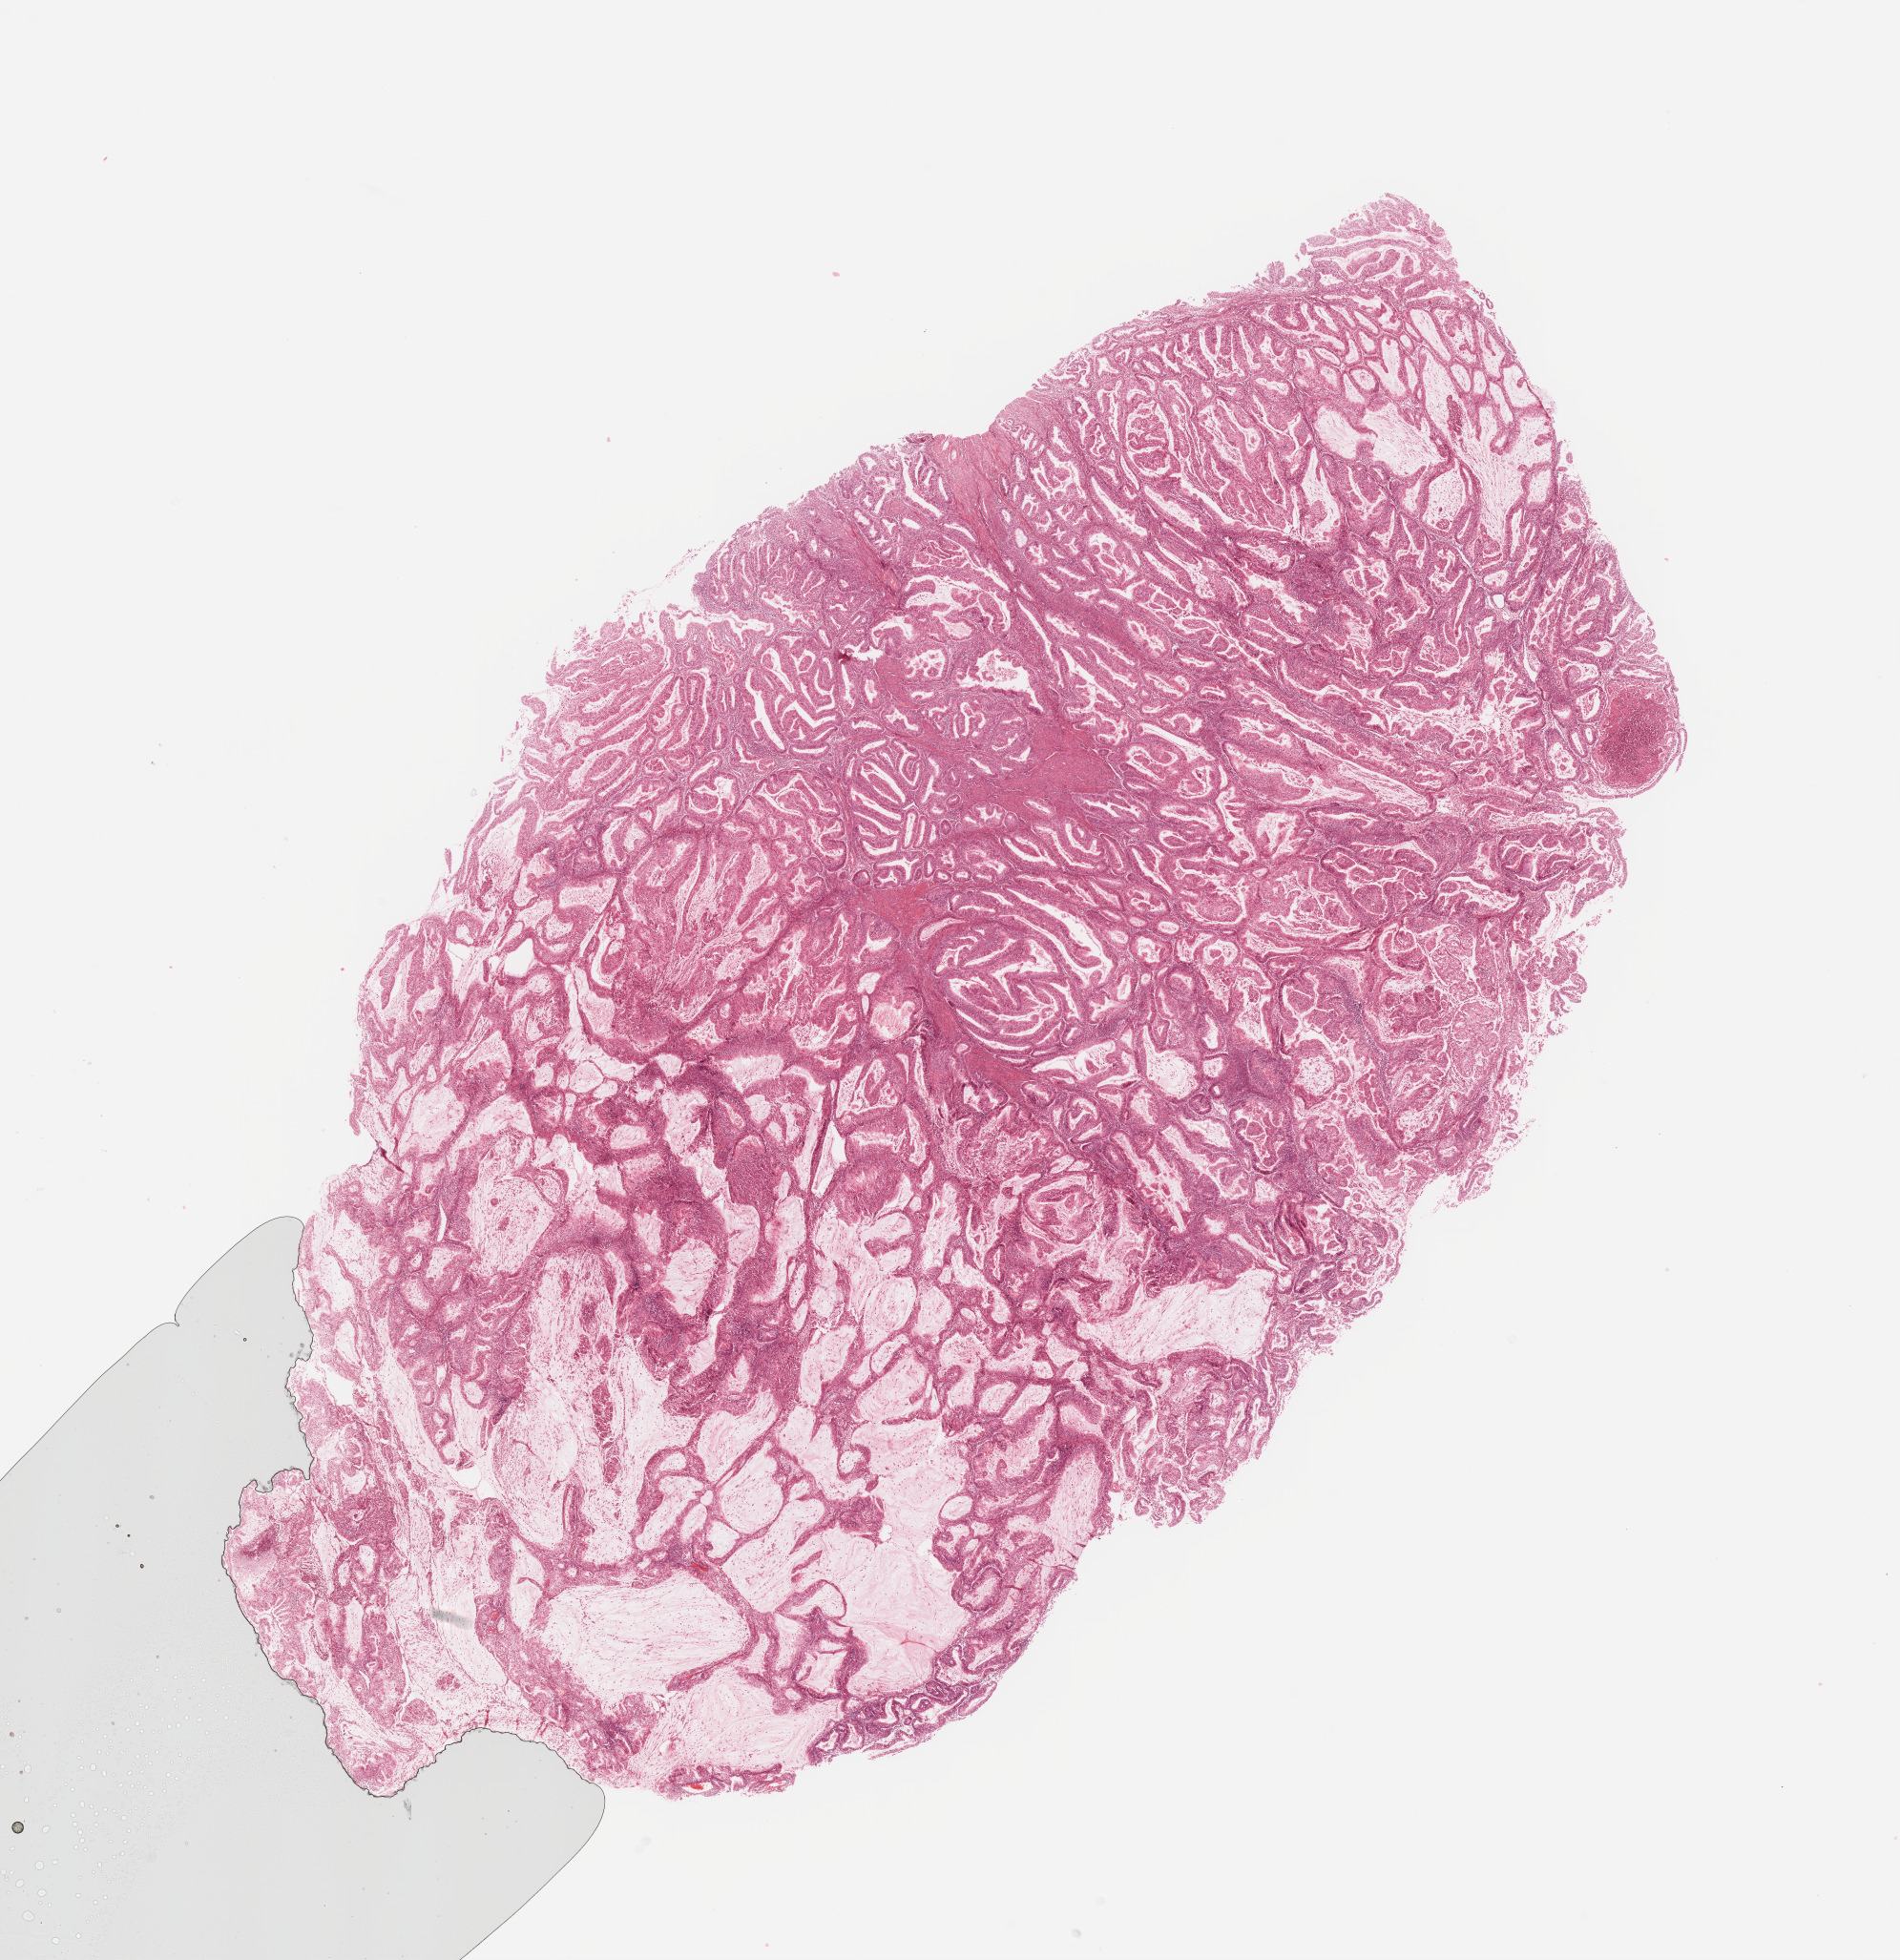
Whole-slide histology image, Hematoxylin and eosin (H&E) stained — shown as a low-resolution overview of the whole scanned area (about 15.8 x 16.2 mm, slide scanned at 20x), tumour tissue sample, uterus. Patient: female, age 57 years. Histologic grade: G1 (well differentiated).
• AJCC pathologic stage: I
• histologic diagnosis: Endometrioid adenocarcinoma, NOS